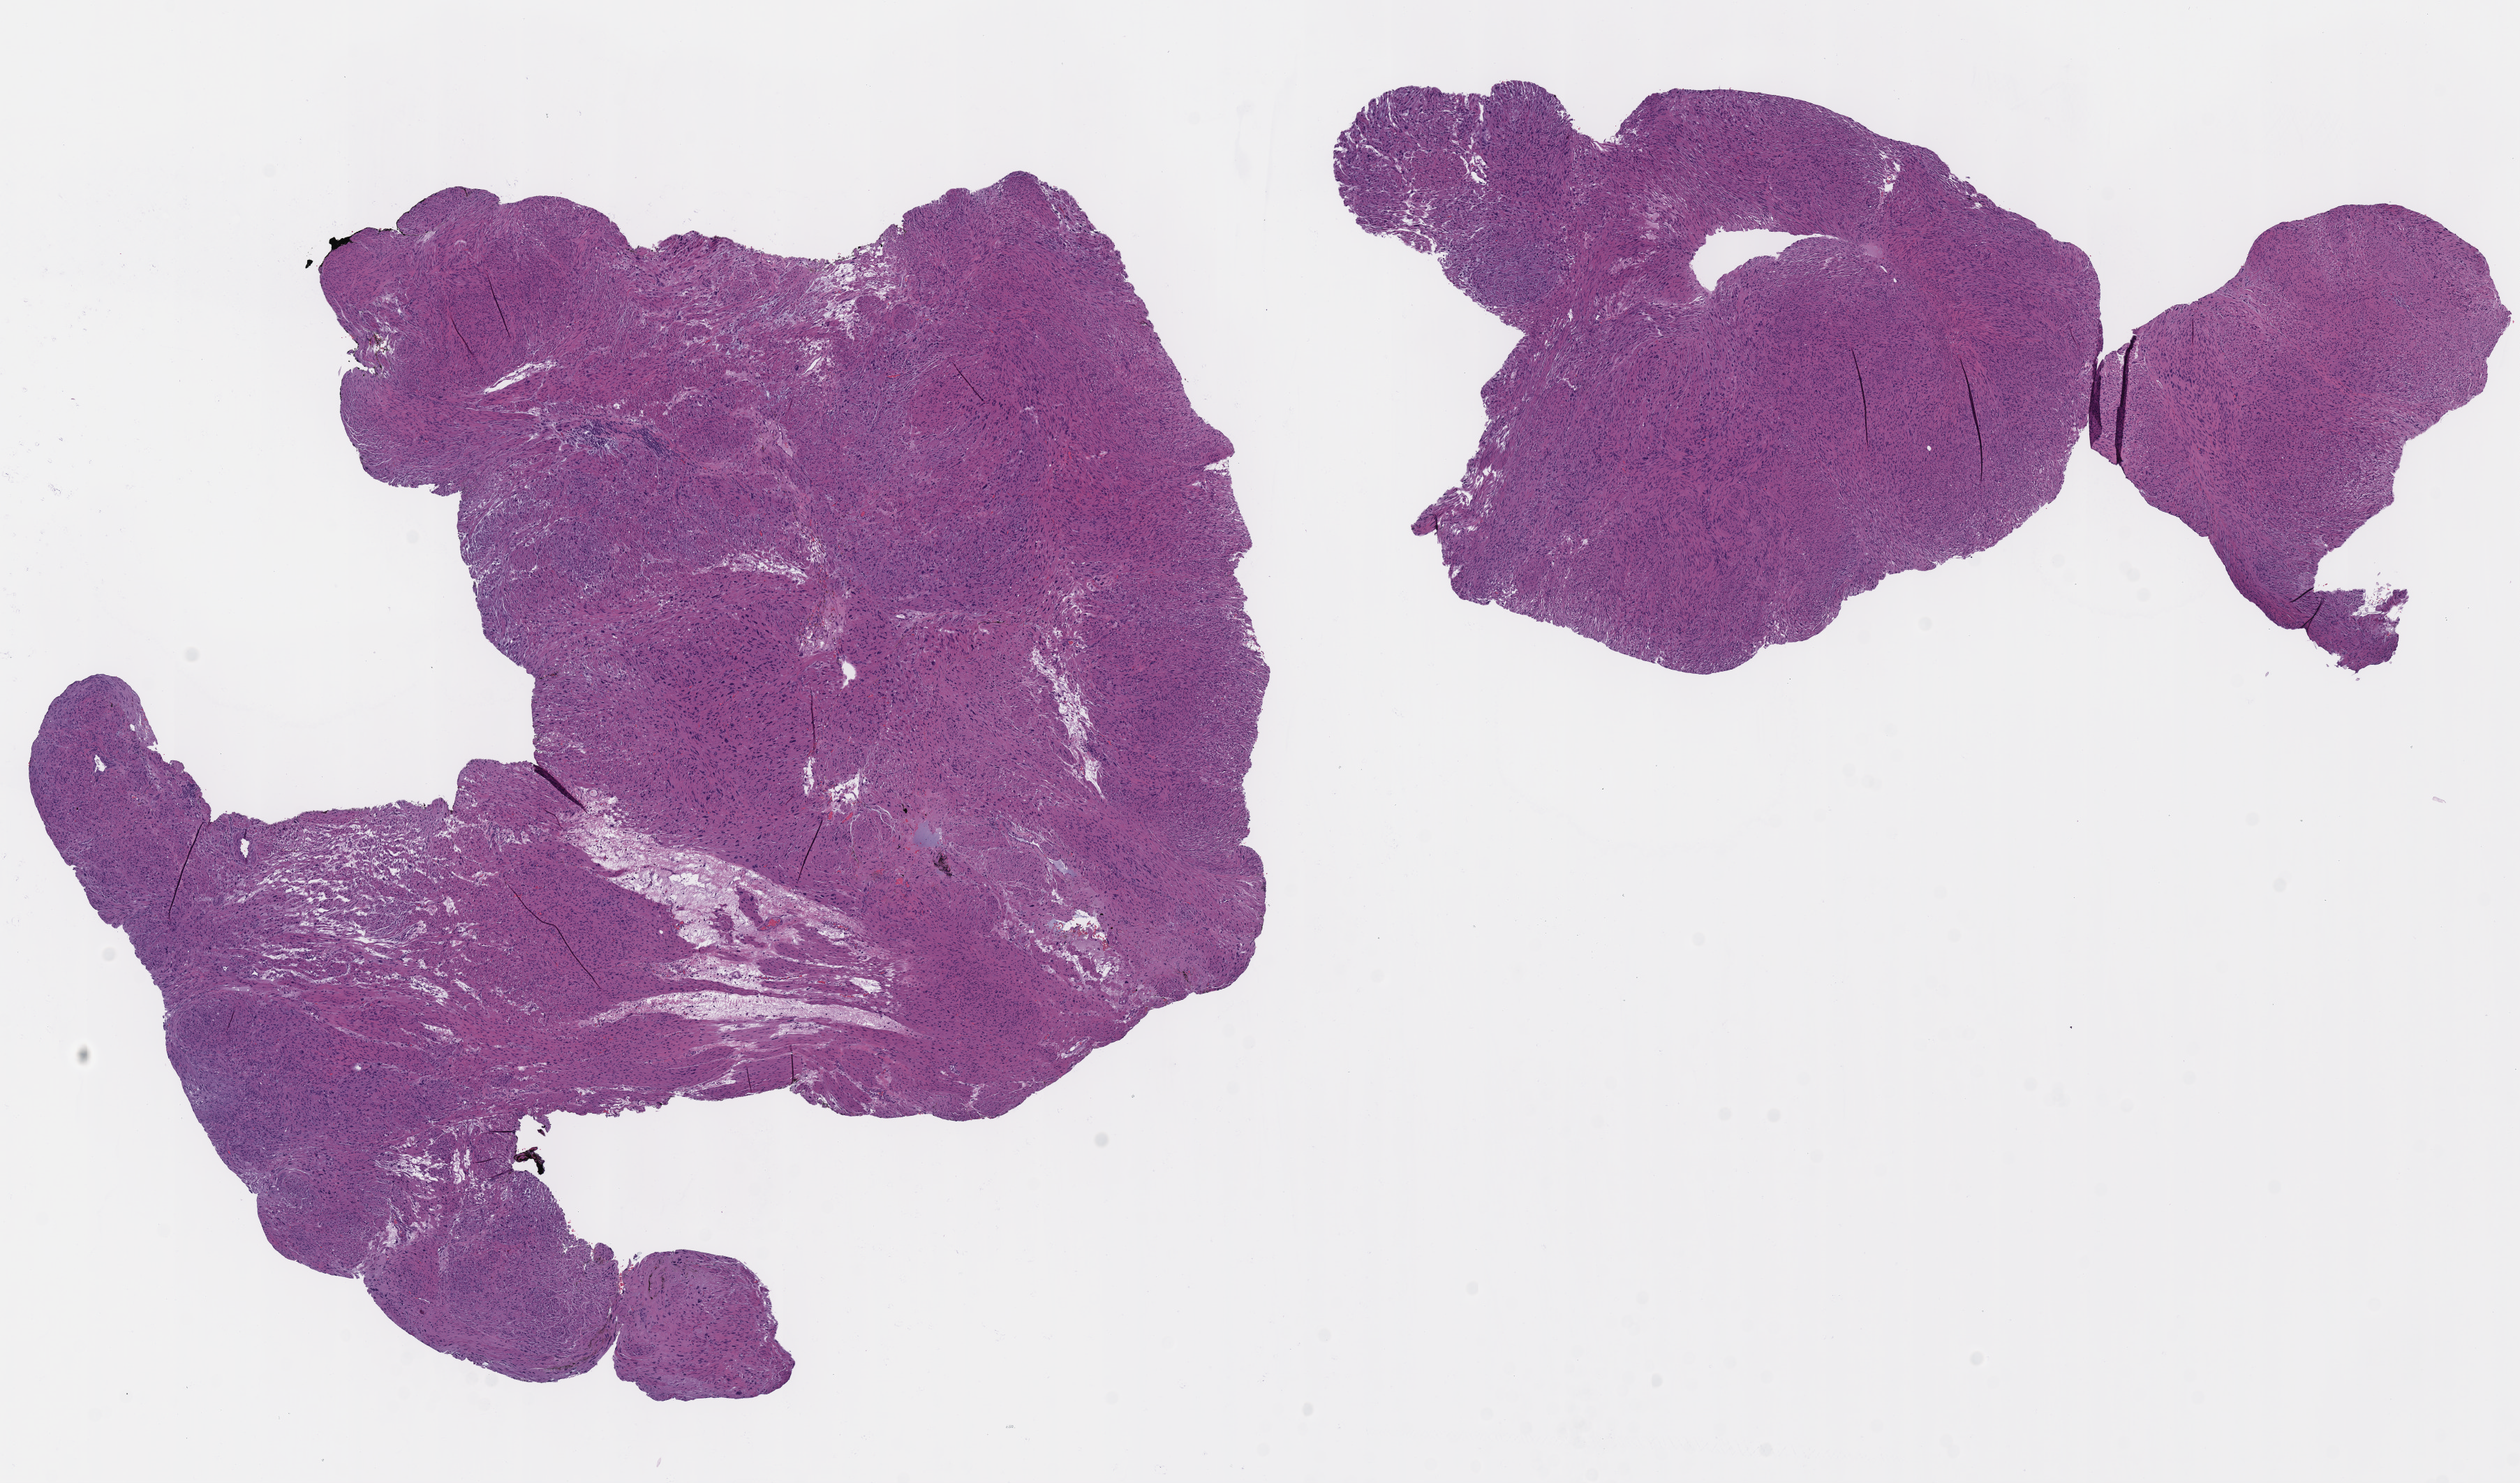
Digitized Hematoxylin and eosin (H&E) stained tissue section (whole slide), shown as a low-resolution overview of the whole scanned area (about 14.2 x 8.4 mm); FFPE section; primary tumour sample from the retroperitoneum and peritoneum. Male patient; age at initial diagnosis 54 years.
• pathologic diagnosis: Leiomyosarcoma, NOS (retroperitoneum)